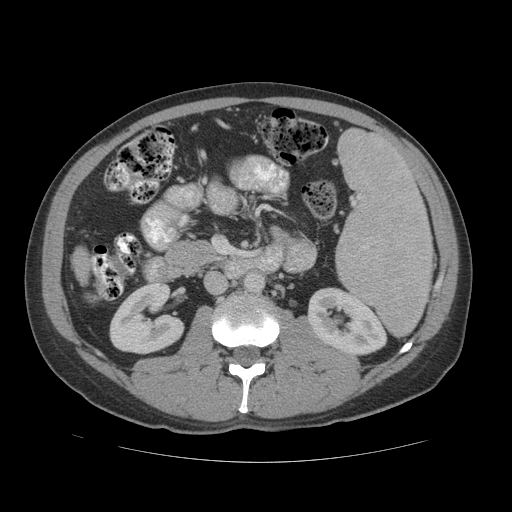
Contrast-enhanced abdominal CT (liver protocol), one axial slice. Reconstruction kernel STANDARD. Soft-tissue window (W 400 / L 40 HU). 512 × 512 image matrix. From the clinical record (not read from this slice): diagnosis: hepatocellular carcinoma (patient treated with transarterial chemoembolisation; whether this scan precedes or follows treatment is not stated here); TNM stage (as recorded): Stage-IVB; Child-Pugh class: B.
Outlined on this slice (semi-automatically segmented with operator editing):
- liver parenchyma outside the tumour (the mass and vessels are separate outlines, so this box may not span the whole liver): bounding box (x1, y1, x2, y2) in pixels: (72, 248, 88, 282)